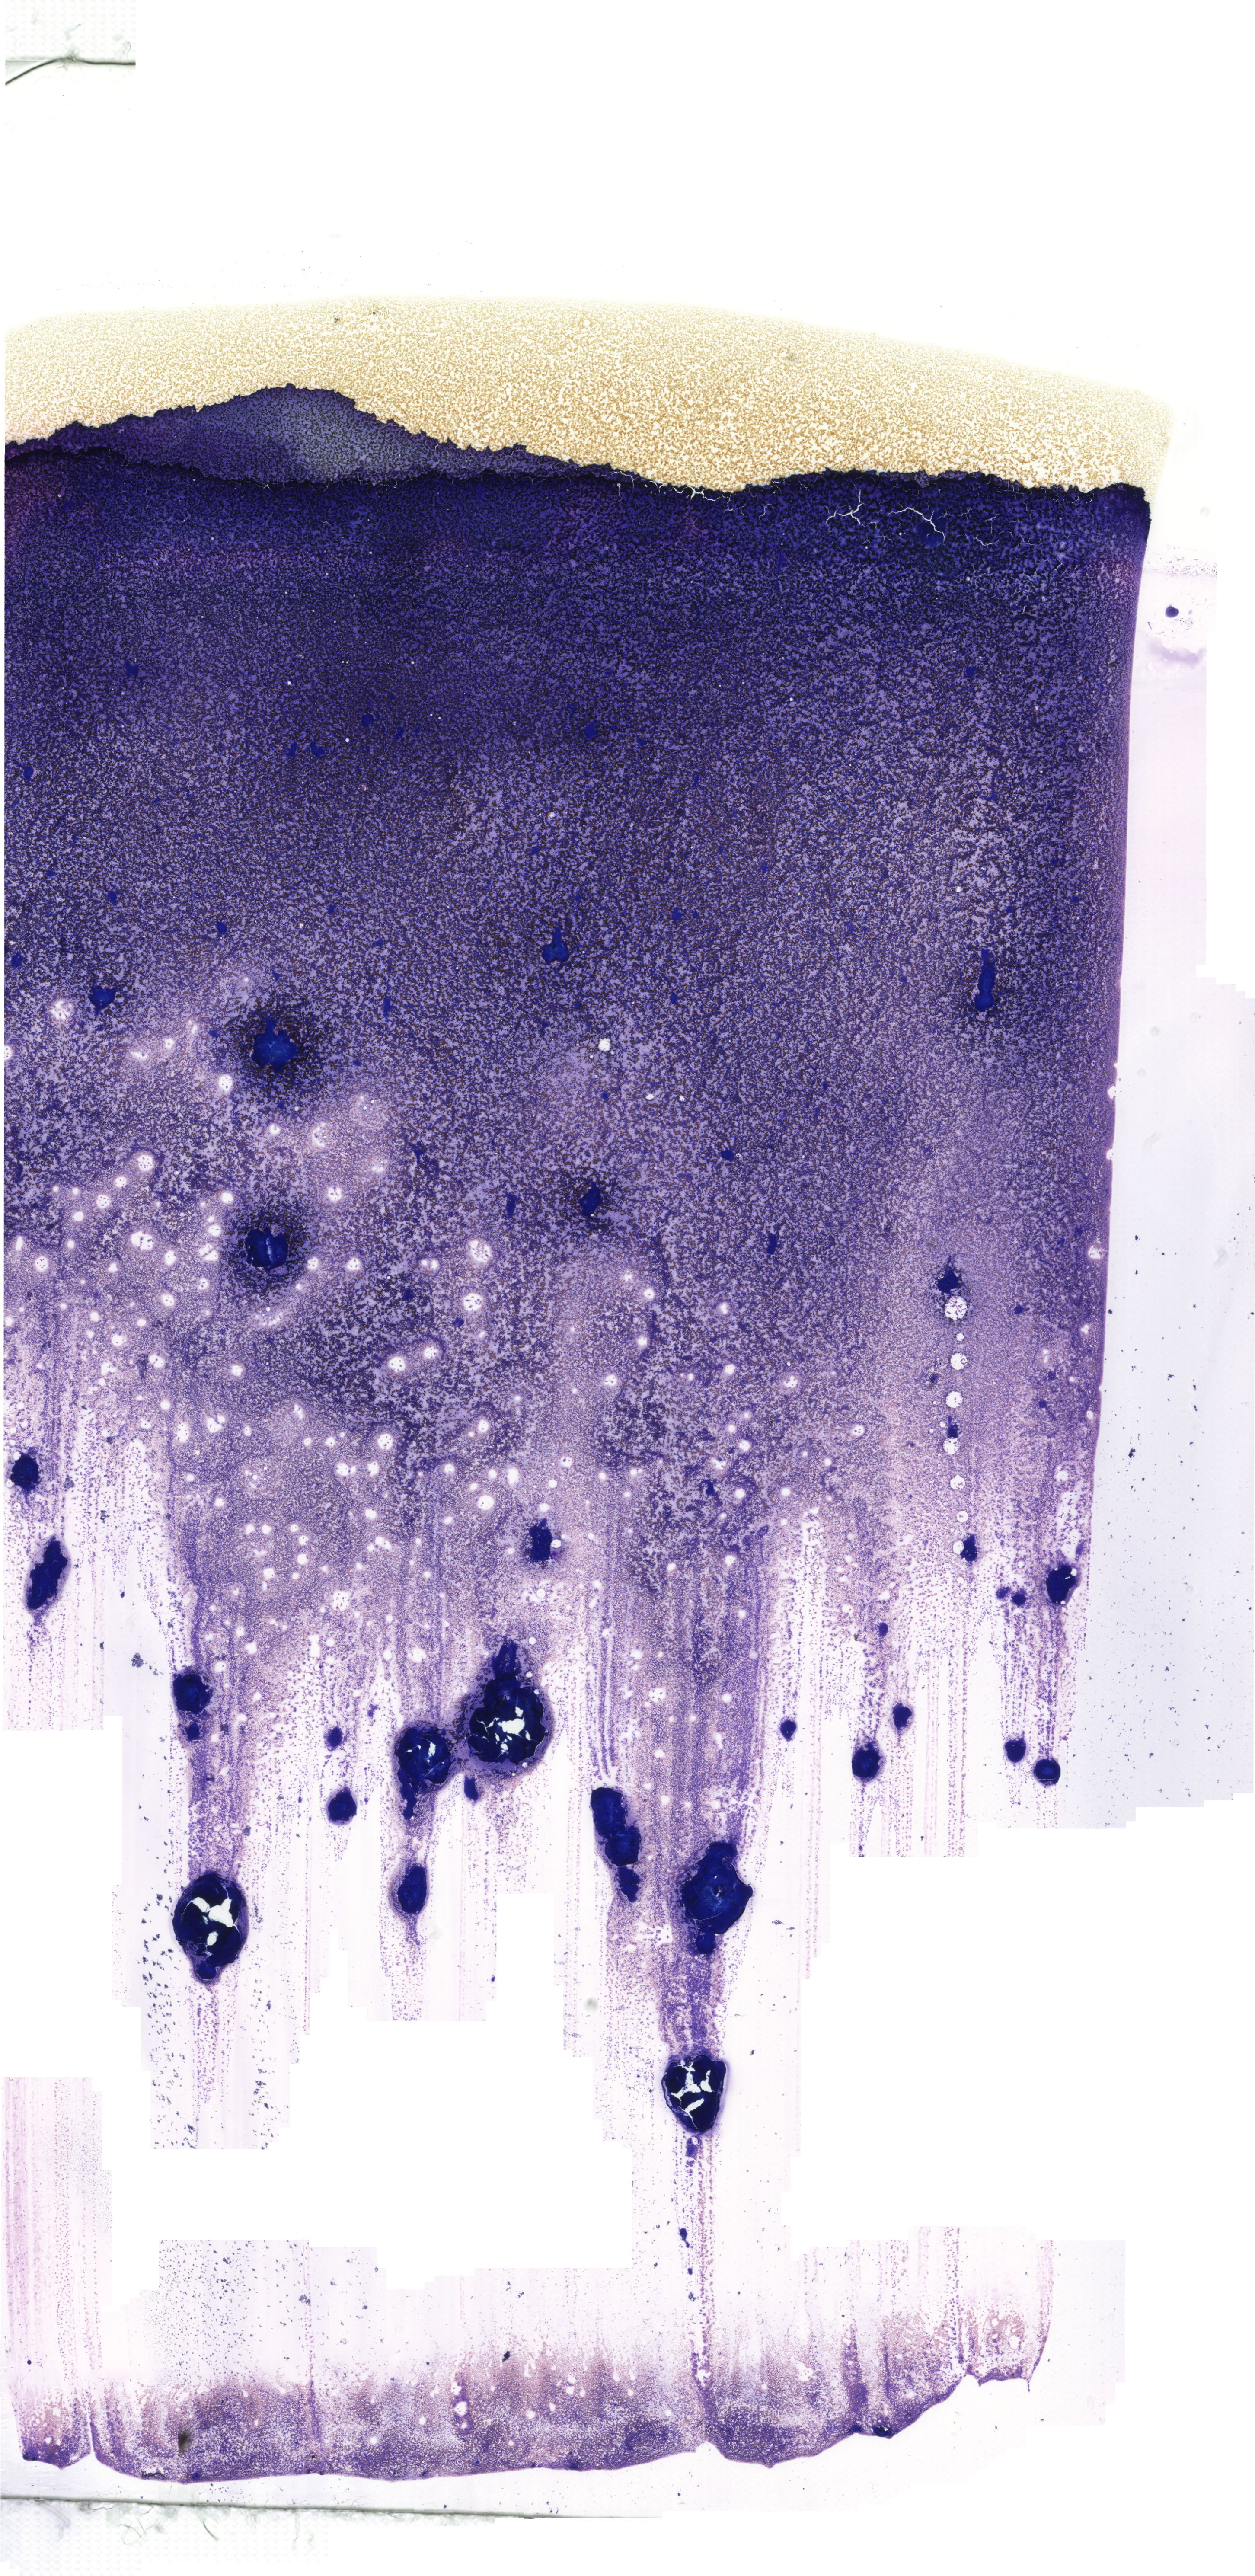
Whole-slide image of a May-Grünwald-Giemsa (MGG)-stained bone marrow aspirate smear, a low-resolution overview of the entire scanned area, about 20.6 x 42.2 mm. Male patient.
Diagnosis: Acute Myeloid Leukemia without Maturation.